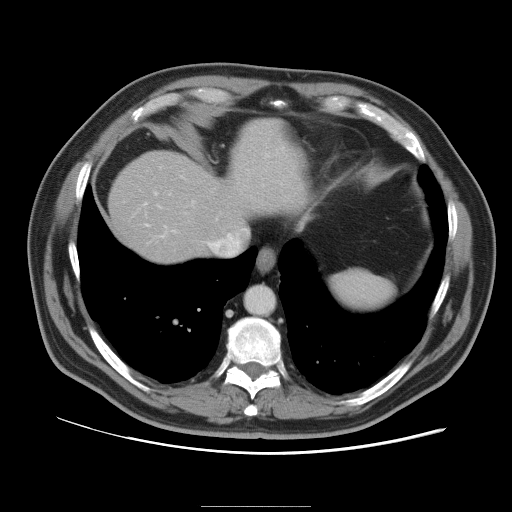
Contrast-enhanced abdominal CT, one axial slice. Slice 87 of 105 in the series (ordered by position). 120 kVp. Intravenous contrast given. Soft-tissue window (W 400 / L 40 HU). 5 mm slice thickness. 512 × 512 image matrix, field of view 399 × 399 mm. Male patient, age 64 years. From the clinical record (not read from this slice): diagnosis: colorectal cancer liver metastases, imaged before liver resection; multiple liver metastases: yes; largest metastasis: 3 cm; disease in both lobes: yes.
Annotated regions visible in this slice (manually delineated by an expert):
- hepatic veins: bounding box <145,194,247,240> (left, top, right, bottom; pixels)
- liver: <109,119,300,263>
- planned liver remnant (the part of the liver to remain after resection): <109,156,228,262>
- portal vein (with intrahepatic branches): <143,175,195,238>